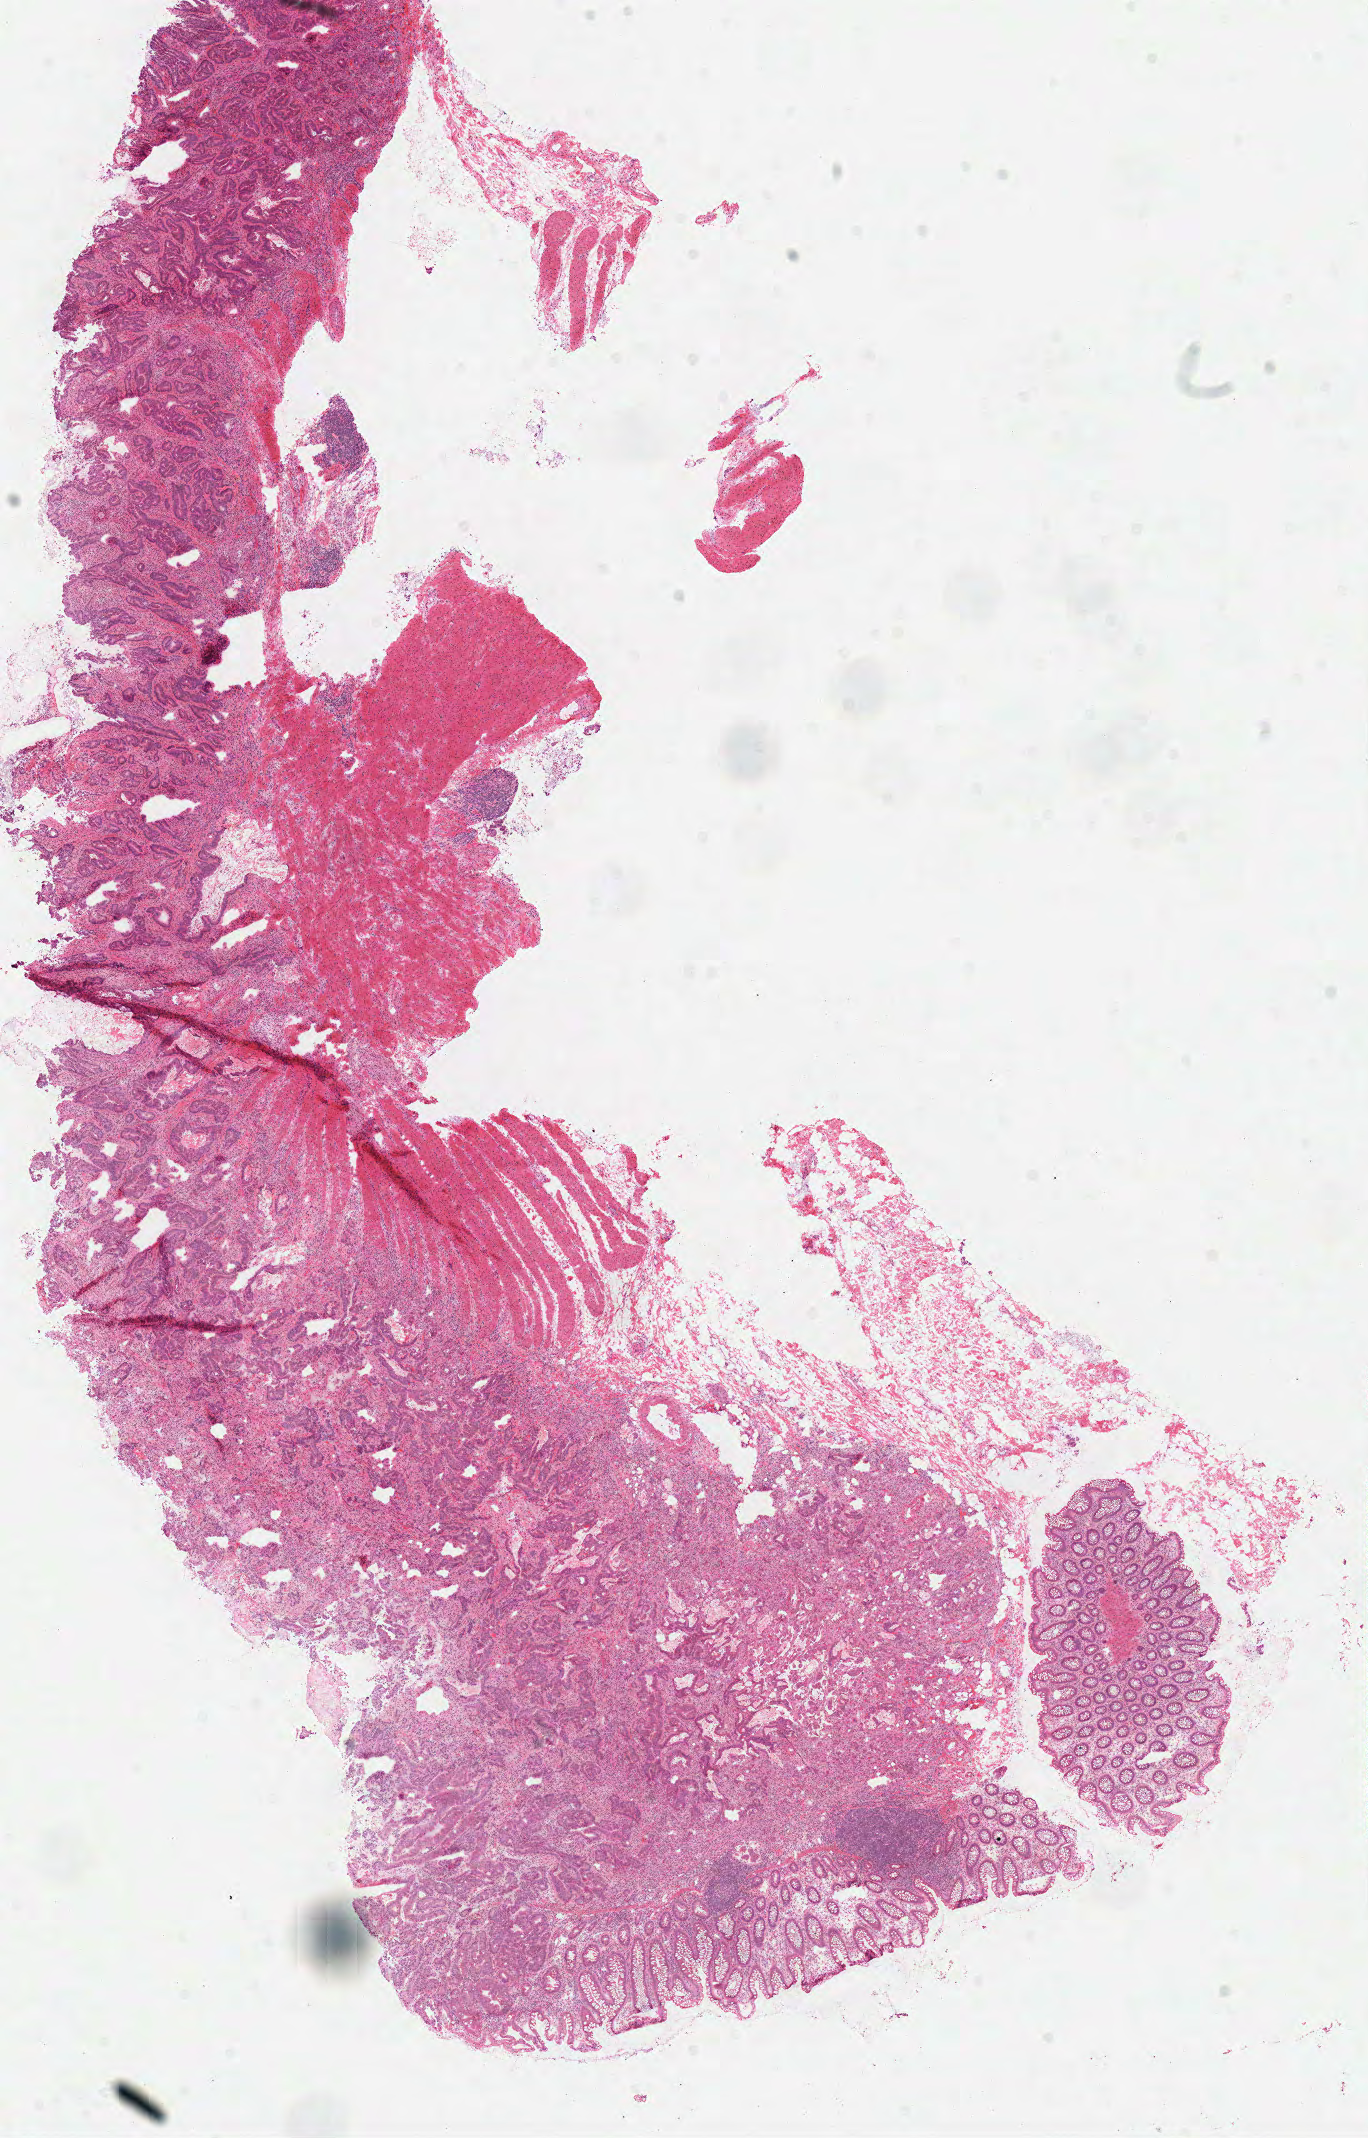
Hematoxylin and eosin (H&E) stained whole-slide image, shown as a low-resolution overview of the whole scanned area (about 10.8 x 16.9 mm). Frozen section from the top of the tissue portion. Sample: primary tumour, colon. Female patient; age at initial diagnosis 84 years. Pathologist review of this section (percent, as recorded): tumour cells 62%, tumour nuclei 70%, normal cells 15%, stromal cells 18%, necrosis 5%.
AJCC pathologic stage: IIA. Lymph nodes positive (case pathology): 0 of 31 examined. Histologic diagnosis: Adenocarcinoma, NOS.